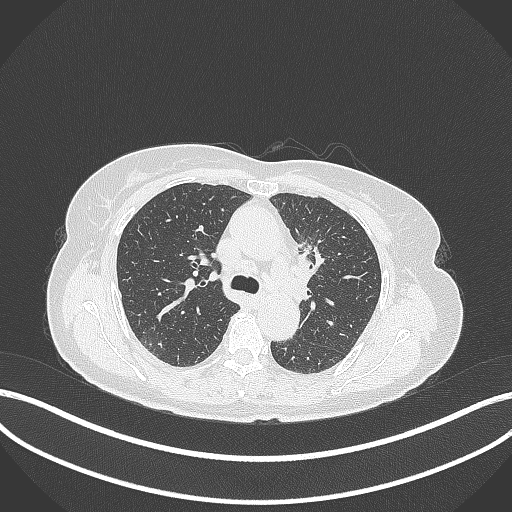
Chest CT, one axial slice; position 224 of 369 along the scan axis; 120 kVp; lung window (W 1500 / L -600 HU); 512 × 512 image matrix. Female patient, age 65 years. From the clinical record (not read from this slice): clinical TNM (as recorded): T2a N0 M0; histopathological grade: G2-3.
Structures marked on this image (bounding box drawn by a radiologist):
- lung tumour (recorded histology: adenocarcinoma): bounding box [x1, y1, x2, y2] px = [296, 233, 326, 280]